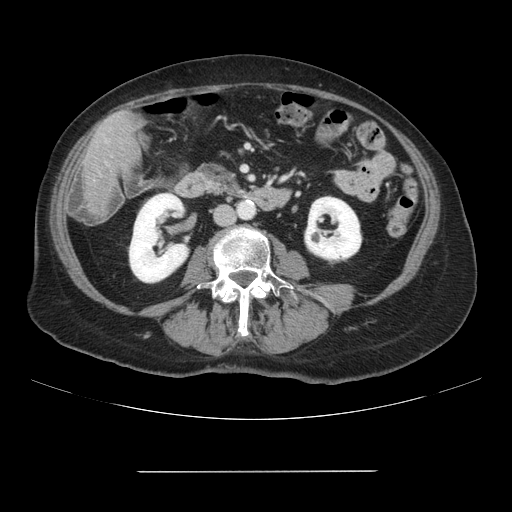
Contrast-enhanced abdominal CT, one axial slice. Position 12 of 111 along the scan axis. 120 kVp. Intravenous contrast given. Soft-tissue window (W 400 / L 40 HU). 2.5 mm slice thickness. 512 × 512 image matrix. Female patient, age 74 years. Case-level facts recorded for this patient, not image findings: diagnosis: colorectal cancer liver metastases, imaged before liver resection.
Outlined on this slice (manually delineated by an expert):
- liver: box from (x=84, y=113) to (x=140, y=216) px